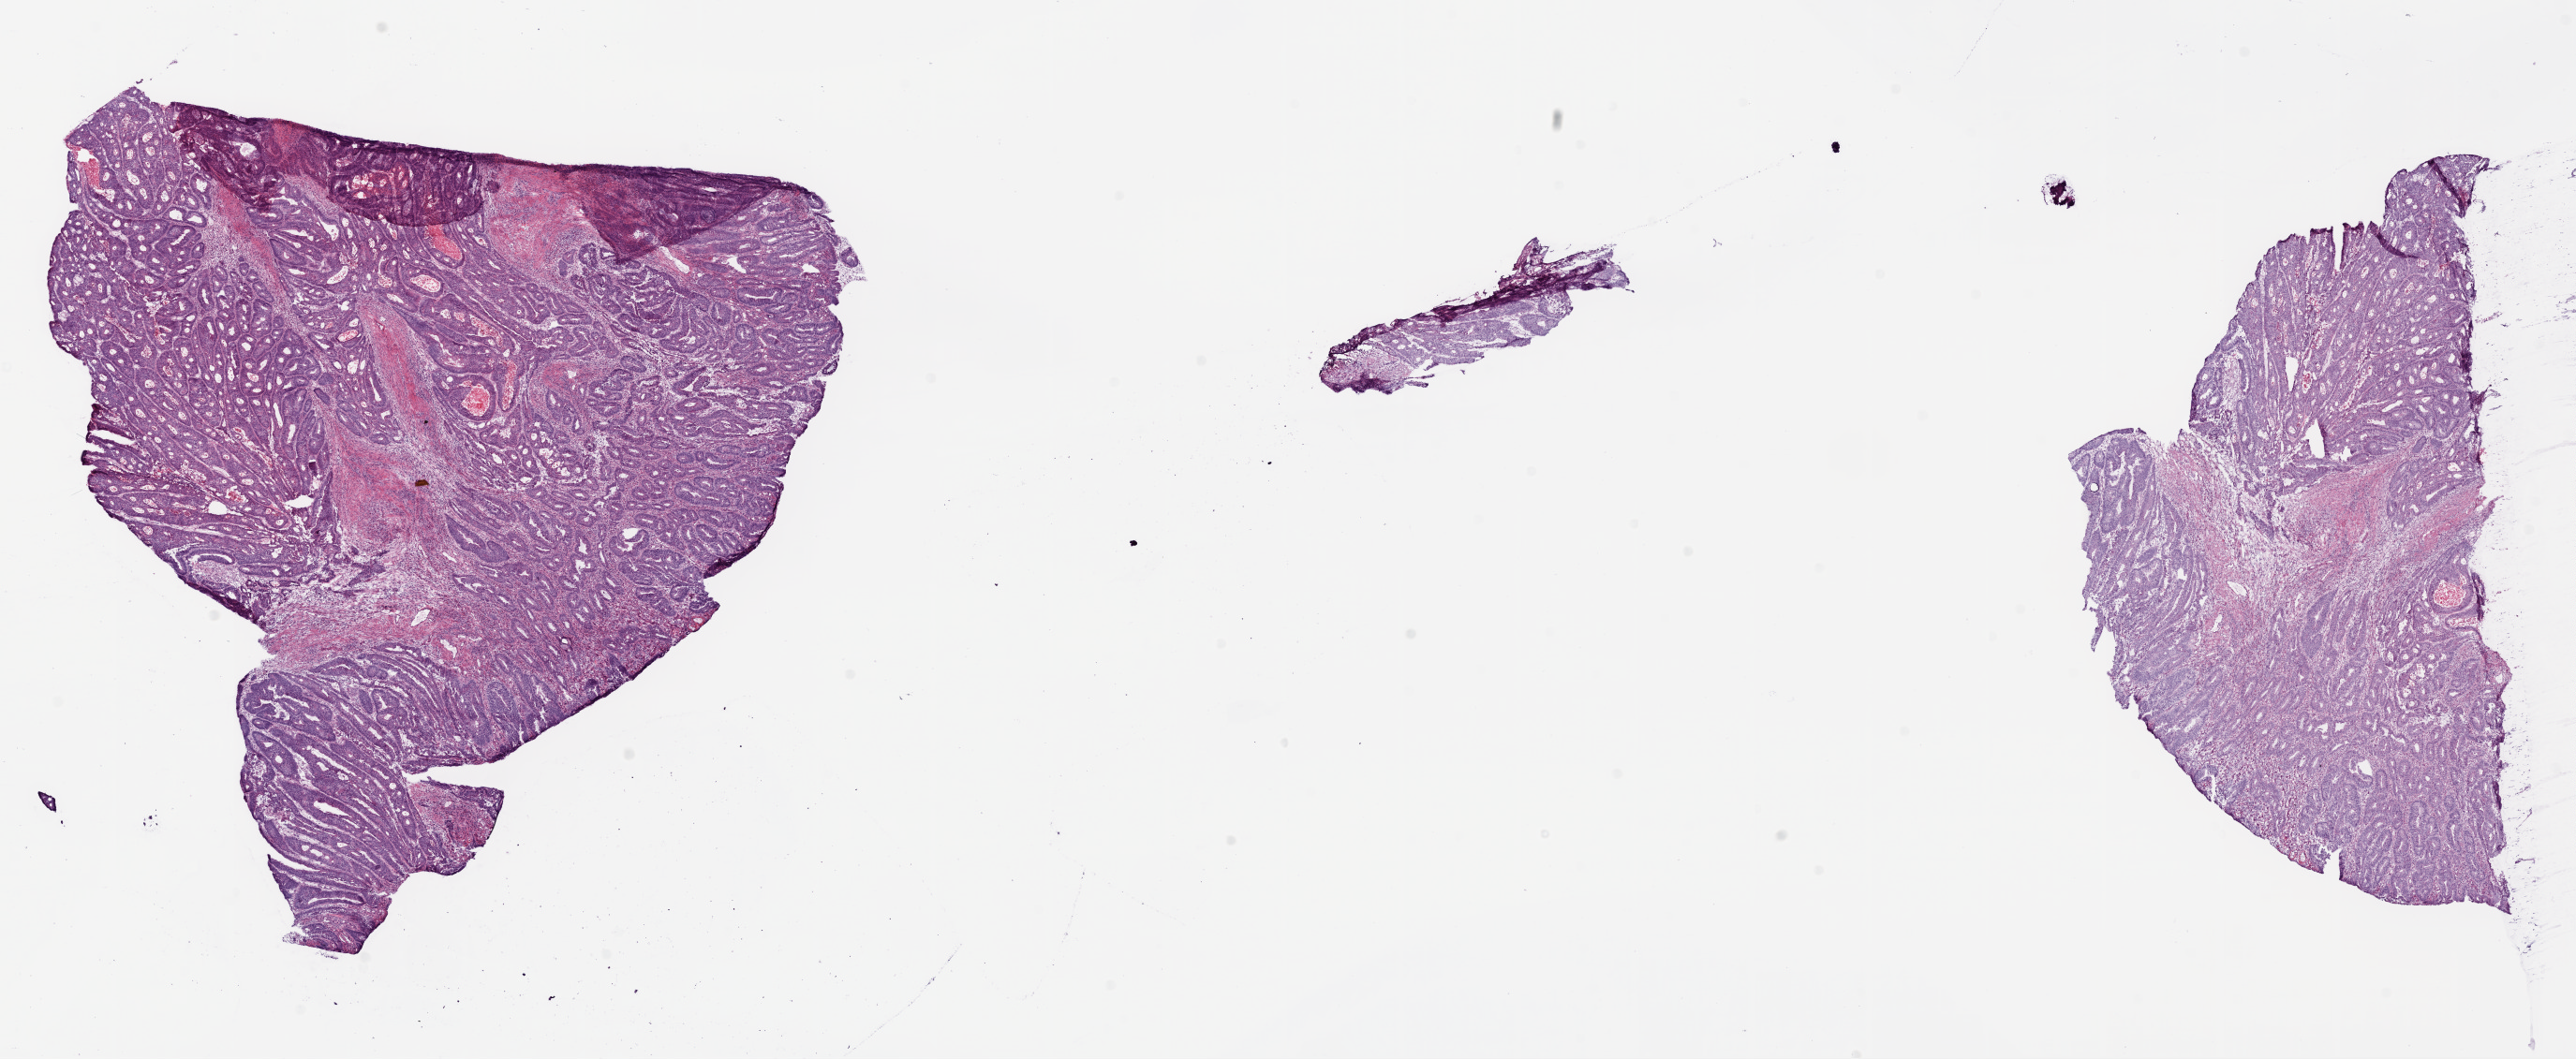
Hematoxylin and eosin (H&E) stained whole-slide image, low-resolution overview of the scanned area, about 22.1 x 9.1 mm. Frozen section from the bottom of the tissue portion. Primary tumour sample from the rectum. Male patient; age at initial diagnosis 65 years. Composition of this section per pathologist review: tumour cells 84%, tumour nuclei 80%, normal cells 0%, stromal cells 8%, necrosis 8%.
- AJCC pathologic stage: IIA (6th edition)
- lymph nodes positive (case pathology): 0 of 15 examined
- pathologic diagnosis: Adenocarcinoma, NOS